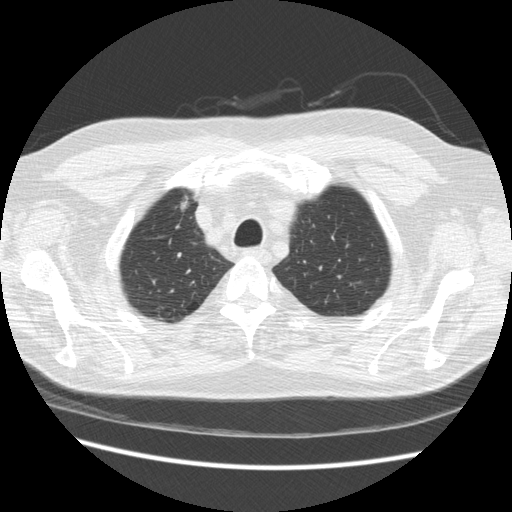
Low-dose screening chest CT, one axial slice; slice 194 of 234 in the series (ordered by position); reconstruction kernel STANDARD; 120 kVp; lung window (W 1500 / L -600 HU); 2.5 mm slice thickness; 512 × 512 image matrix.
Structures marked on this image (expert manual segmentation):
- lesion 1 (tumor, upper lobe of right lung): box from (x=180, y=195) to (x=189, y=211) px